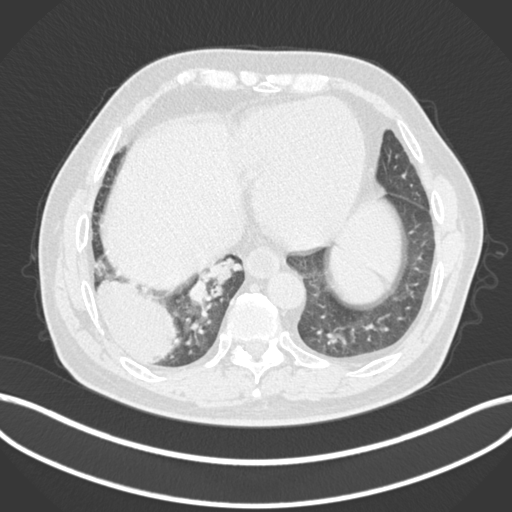
Chest CT, one axial slice. Slice 32 of 200 in the series (ordered by position). 120 kVp. Lung window (W 1500 / L -600 HU). 1 mm slice thickness. 512 × 512 image matrix, field of view 400 × 400 mm. Patient: male, 59 years.
Outlined on this slice (bounding box drawn by a radiologist):
- lung tumour (recorded histology: adenocarcinoma): box from (x=91, y=275) to (x=182, y=367) px